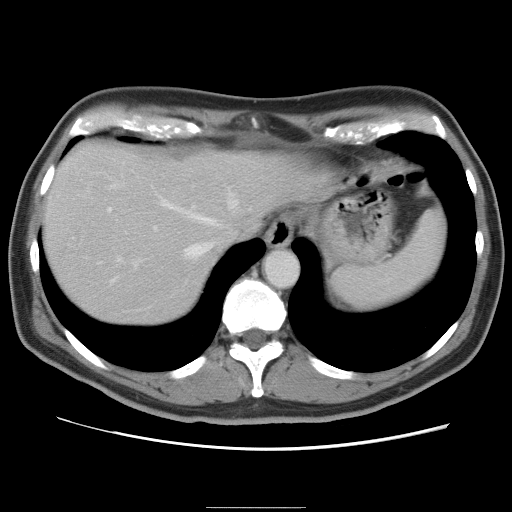
Contrast-enhanced abdominal CT, one axial slice; 120 kVp; intravenous contrast given; soft-tissue window (W 400 / L 40 HU); 5 mm slice thickness; 512 × 512 image matrix, field of view 363 × 363 mm. Male patient, age 63 years. Case-level facts recorded for this patient, not image findings: diagnosis: colorectal cancer liver metastases, imaged before liver resection; multiple liver metastases: no; largest metastasis: 9 cm; disease in both lobes: no.
Annotated regions visible in this slice (outlined manually by an expert reader):
- hepatic veins: bounding box (x1, y1, x2, y2) in pixels: (97, 182, 239, 264)
- liver: (43, 143, 317, 325)
- planned liver remnant (the part of the liver to remain after resection): (43, 165, 216, 325)
- portal vein (with intrahepatic branches): (106, 206, 159, 285)